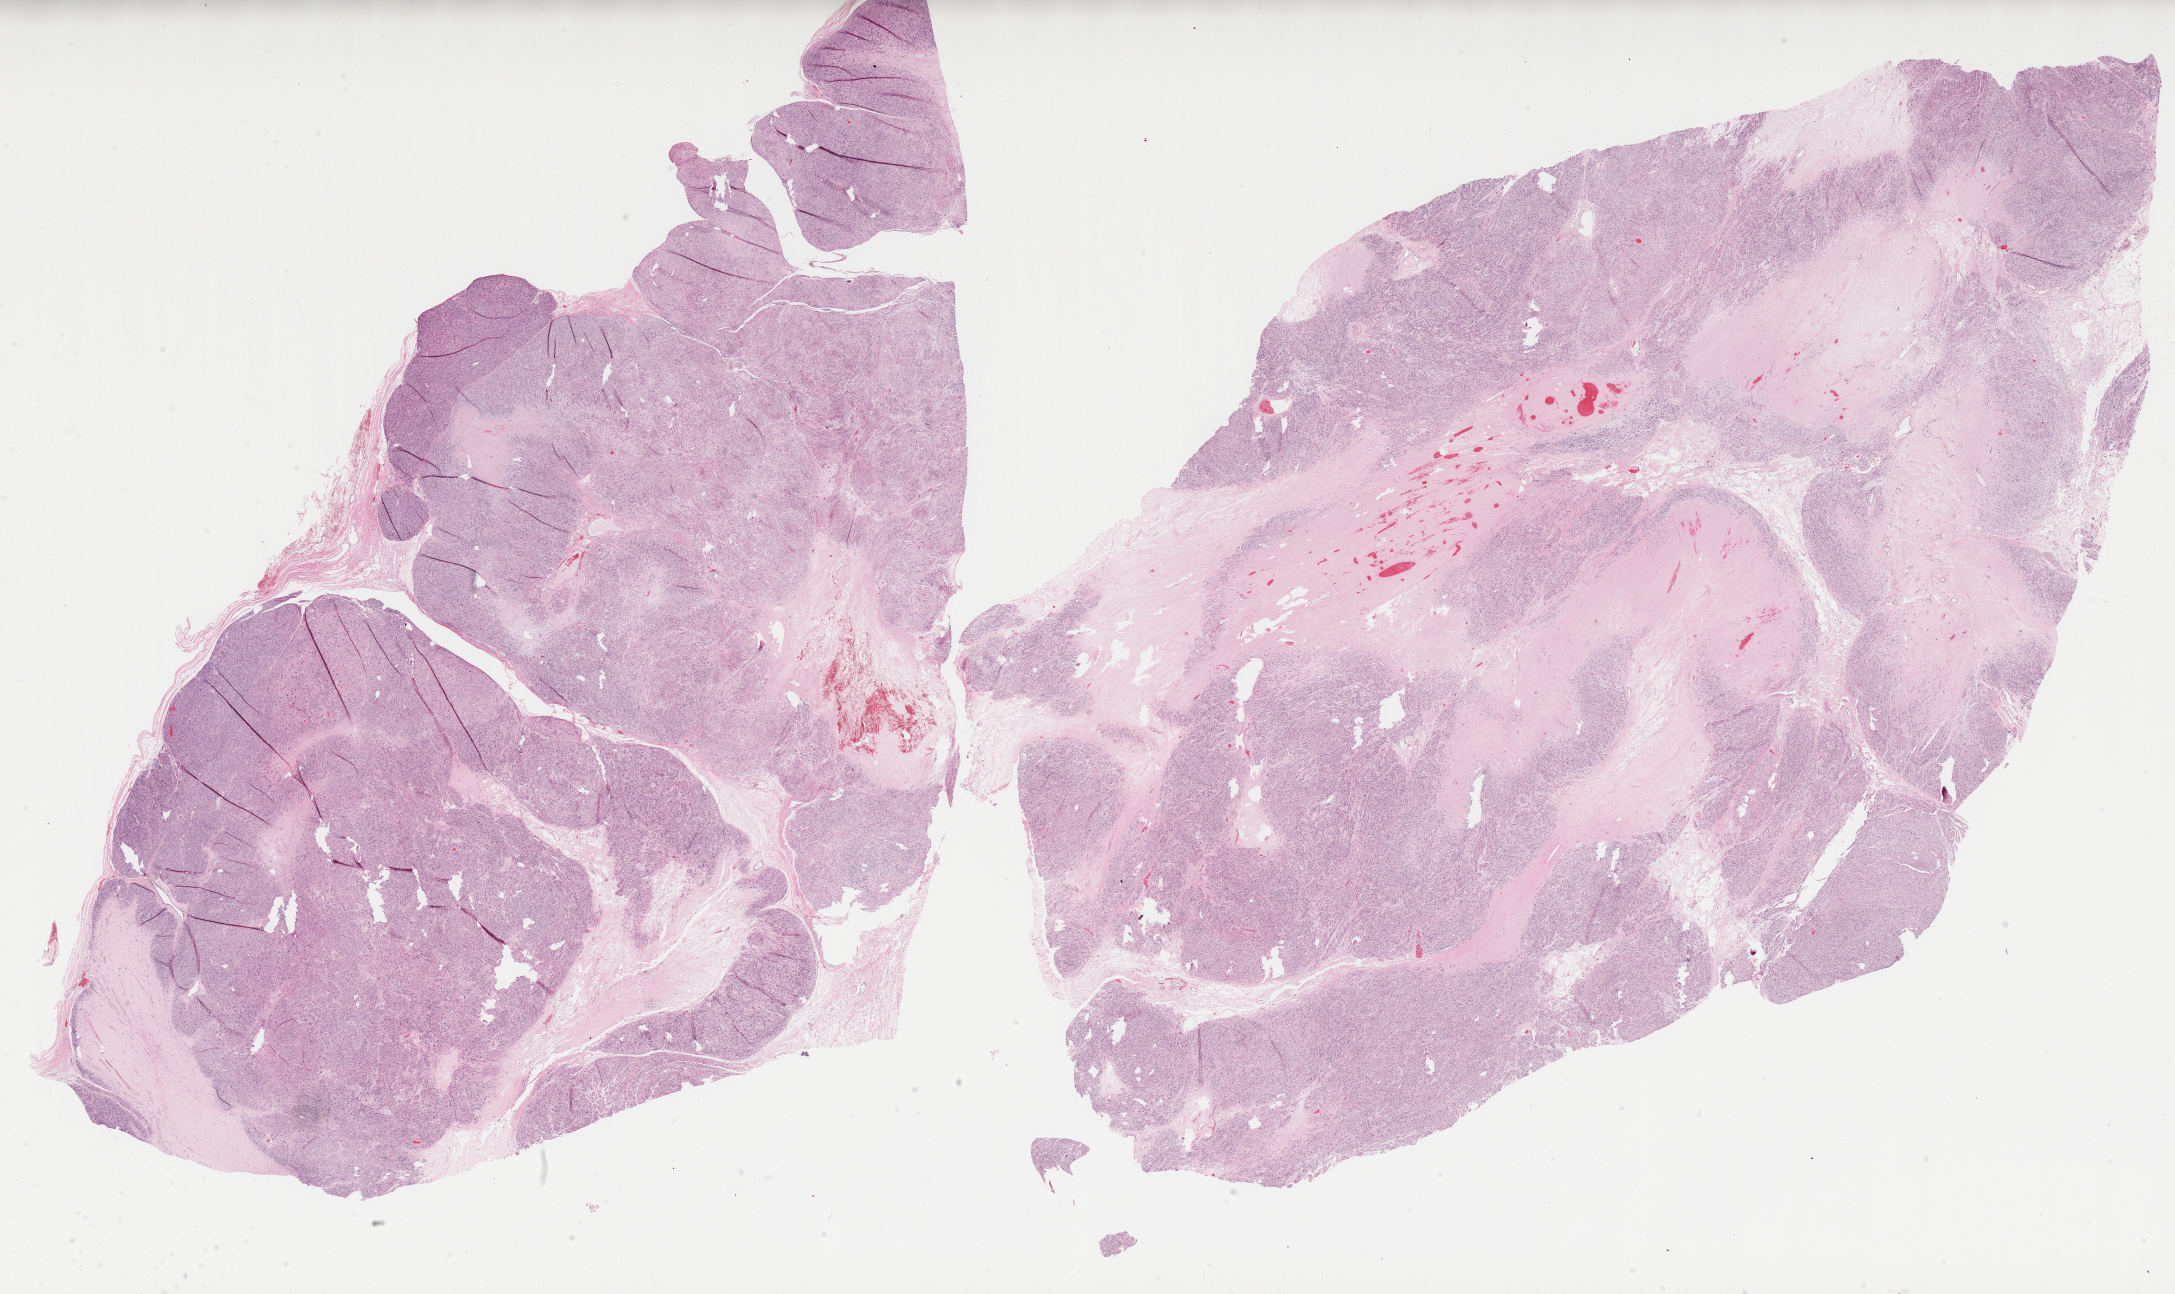
Whole-slide histology image, H&E-stained, low-resolution overview of the scanned area, about 34.7 x 20.6 mm; FFPE section; primary tumour sample from the retroperitoneum and peritoneum. Male patient; age at initial diagnosis 74 years.
- histologic diagnosis: Leiomyosarcoma, NOS